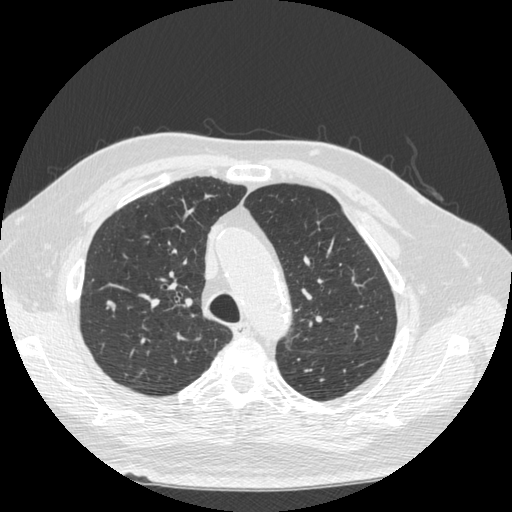
Chest CT (low-dose screening protocol), one axial image. Second screening round (one year after baseline). Lung window (W 1500 / L -600 HU). 1.25 mm slice thickness. 120 kVp. 512 × 512 image matrix. Male participant, aged 72 years at enrolment. Former smoker at enrolment.
Expert-annotated lung lesion, bounding box <87,291,124,322> (left, top, right, bottom; pixels). No non-calcified nodule or mass ≥4 mm was recorded by the screening reader at this exam. Official screen result: negative screen, minor abnormalities not suspicious for lung cancer. Lung cancer was diagnosed 449 days after this screen (after the third annual screen): squamous cell carcinoma, NOS, right upper lobe, poorly differentiated (G3), stage IIIA (AJCC 6th edition), 19 mm at pathology.